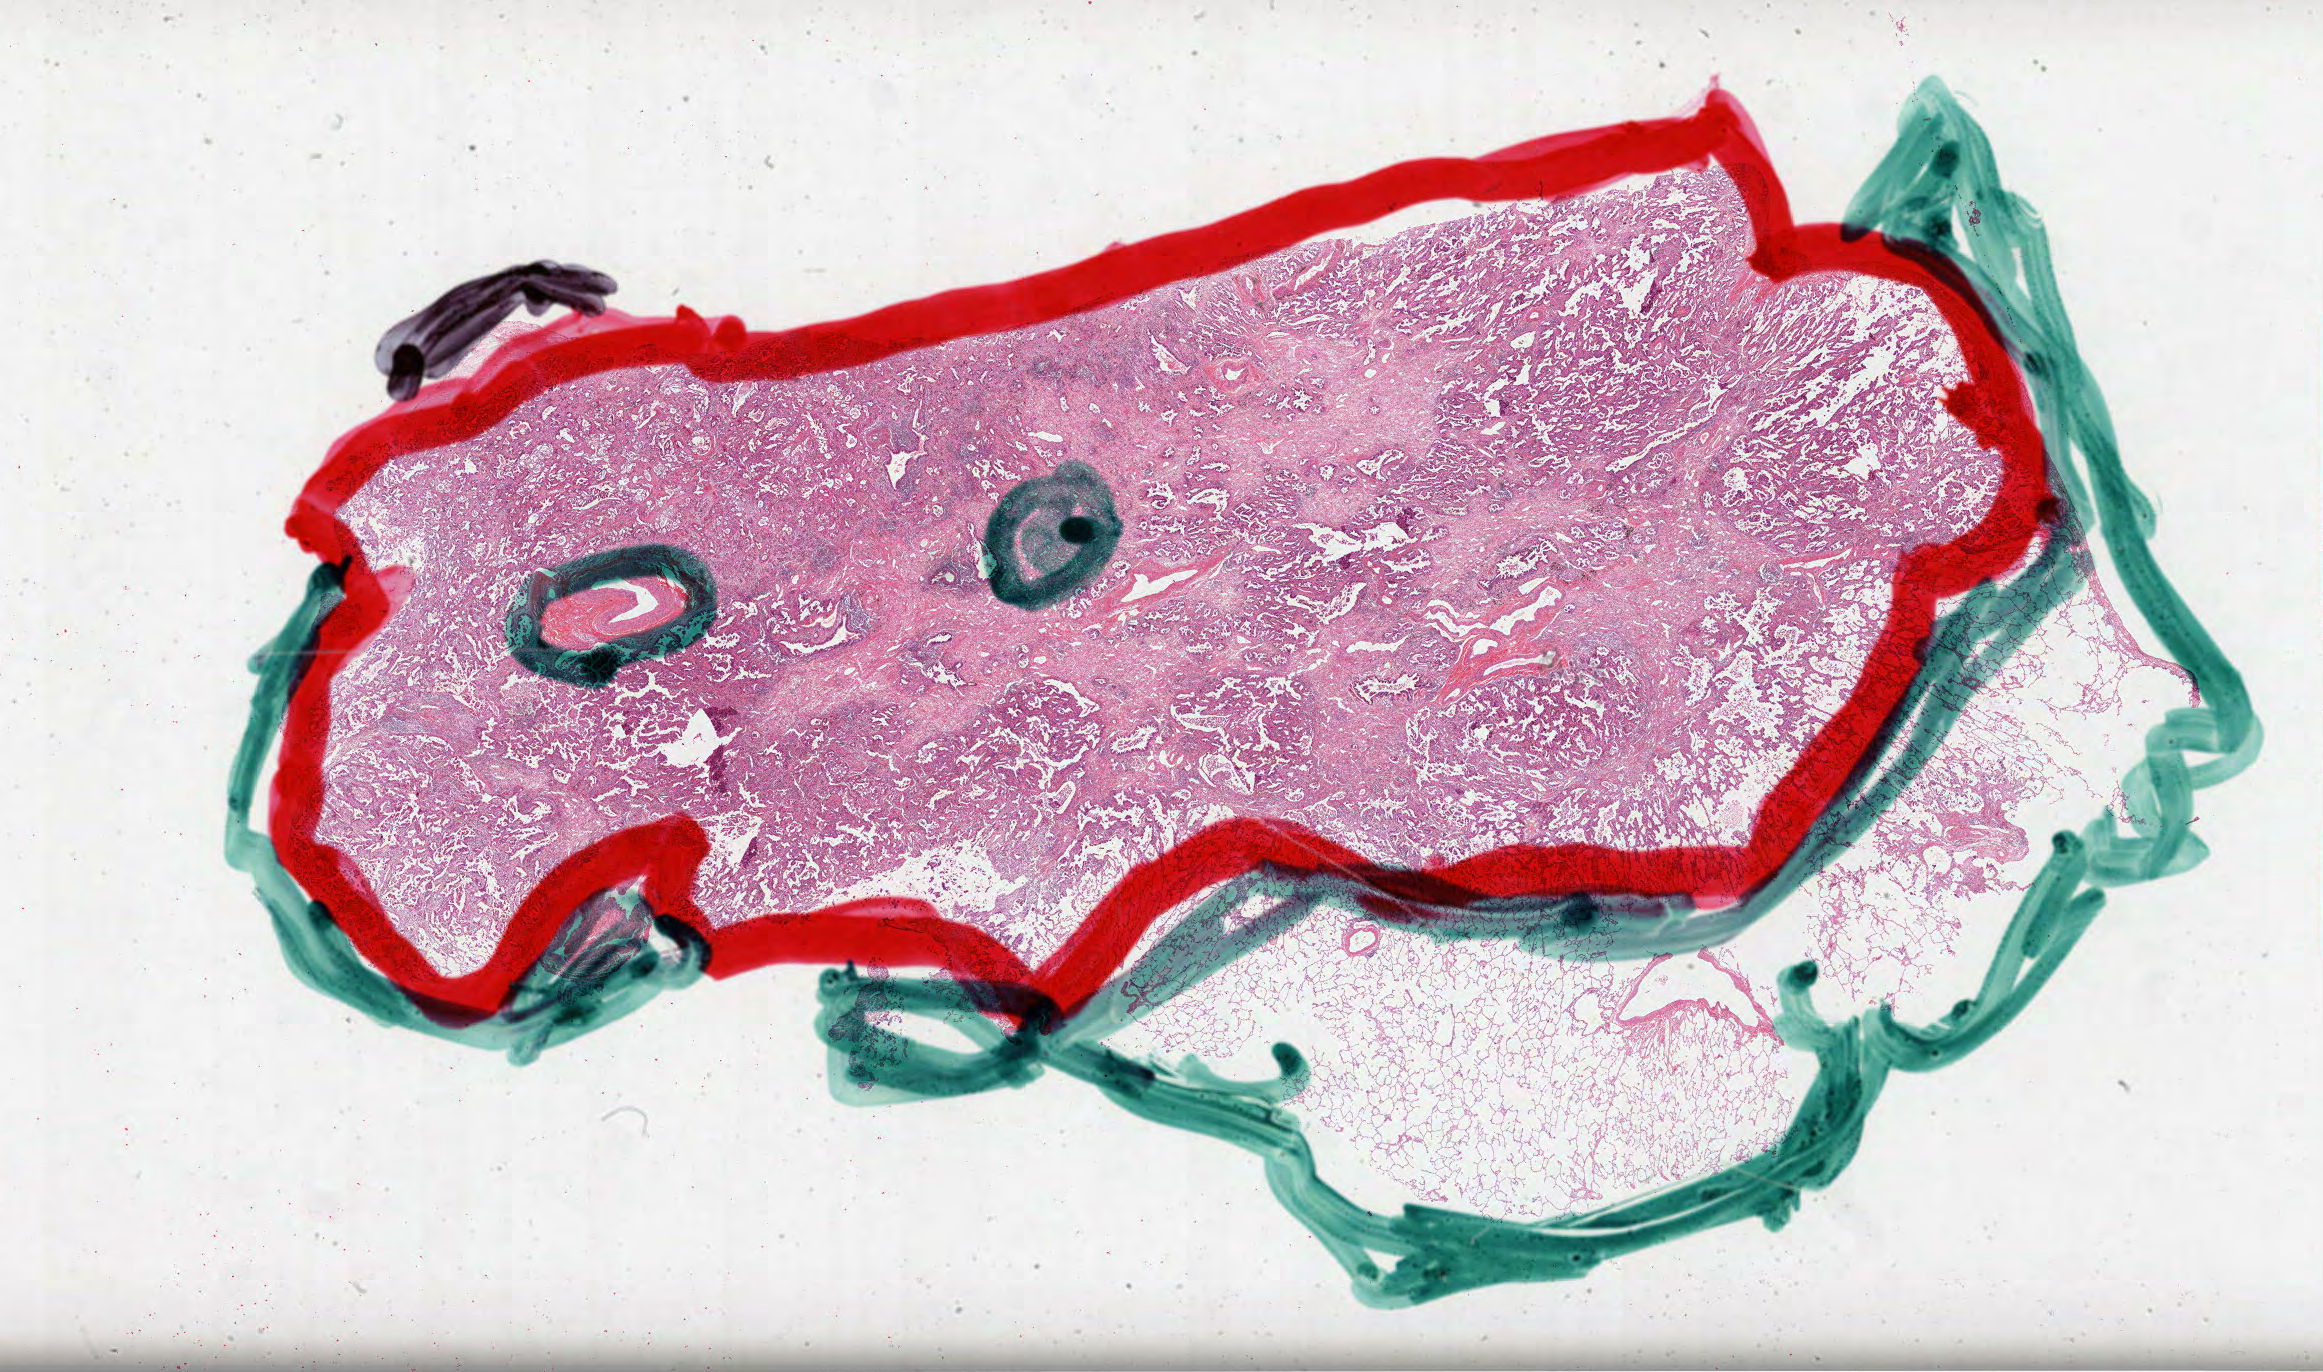
Whole-slide histology image, H&E — whole scanned area (about 37.5 x 22.1 mm) shown as a low-resolution overview. Formalin-fixed paraffin-embedded (FFPE) diagnostic section. Lung, primary tumour sample. Female patient; age at initial diagnosis 54 years.
* diagnosis: Bronchiolo-alveolar carcinoma, non-mucinous (lower lobe, lung)
* AJCC pathologic stage: IIA (7th edition)
* TNM: T2b N0 M0